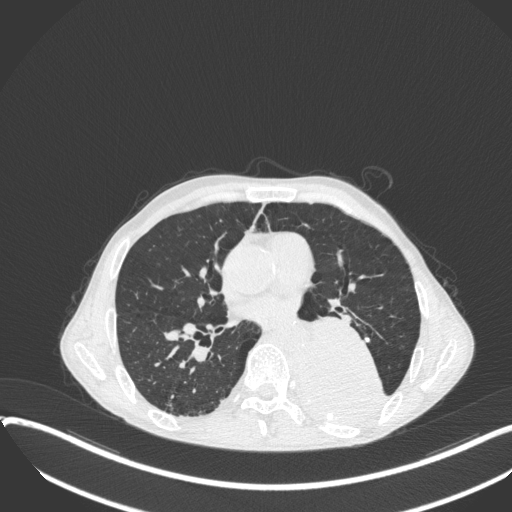
Chest CT, one axial slice; position 187 of 400 along the scan axis; reconstruction kernel B31f; 120 kVp; lung window (W 1500 / L -600 HU); 1 mm slice thickness; 512 × 512 image matrix. Male patient, age 57 years. Case-level facts recorded for this patient, not image findings: clinical TNM (as recorded): T4 N0 M0.
Structures marked on this image (rectangle marked by the reading radiologist):
- lung tumour (recorded histology: squamous cell carcinoma): bounding box (x1, y1, x2, y2) in pixels: (294, 316, 388, 421)